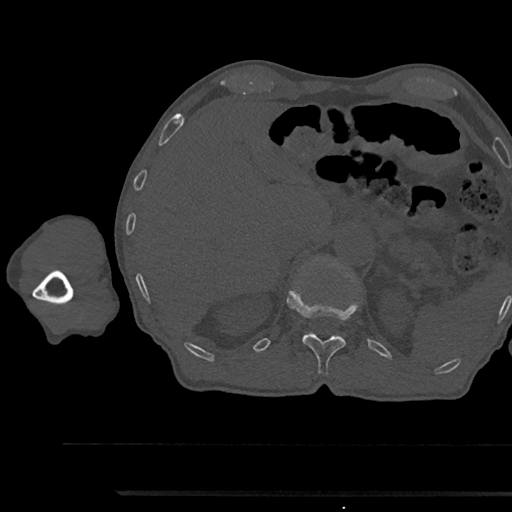
CT including the spine, one axial slice. Slice 697 of 797 in the series (ordered by position). 120 kVp. Bone window (W 1800 / L 400 HU). 0.5 mm slice thickness. 512 × 512 image matrix. Male patient, age 79 years. From the clinical record (not read from this slice): primary cancer: prostate.
Structures marked on this image (semi-automatic segmentation, software-assisted and operator-edited):
- T12 vertebra: bounding box [x1, y1, x2, y2] px = [287, 292, 356, 374]